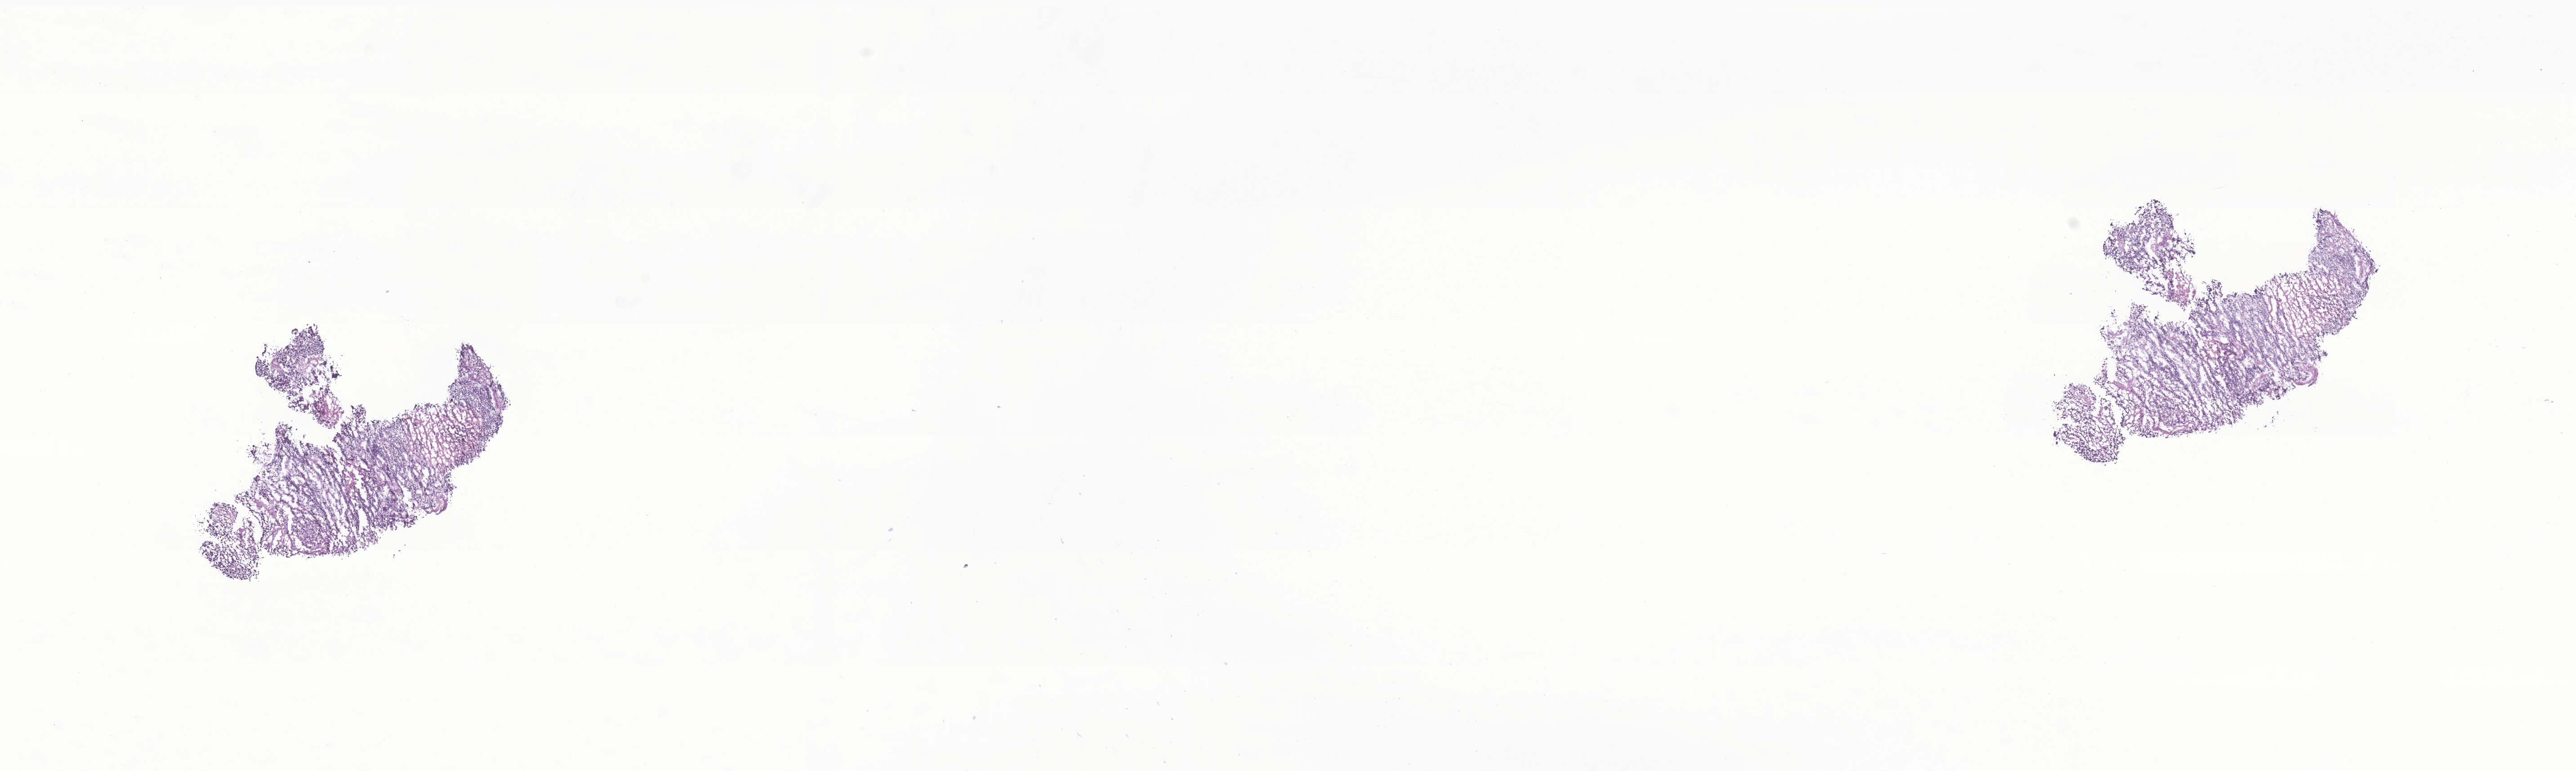
Digitized haematoxylin and eosin-stained section of tumor tissue from the brain — shown as a low-resolution overview of the whole scanned area (about 24.2 x 7.2 mm), frozen section. Male patient, age 118 months (9 years 10 months).
- recorded diagnosis: Medulloblastoma, NOS